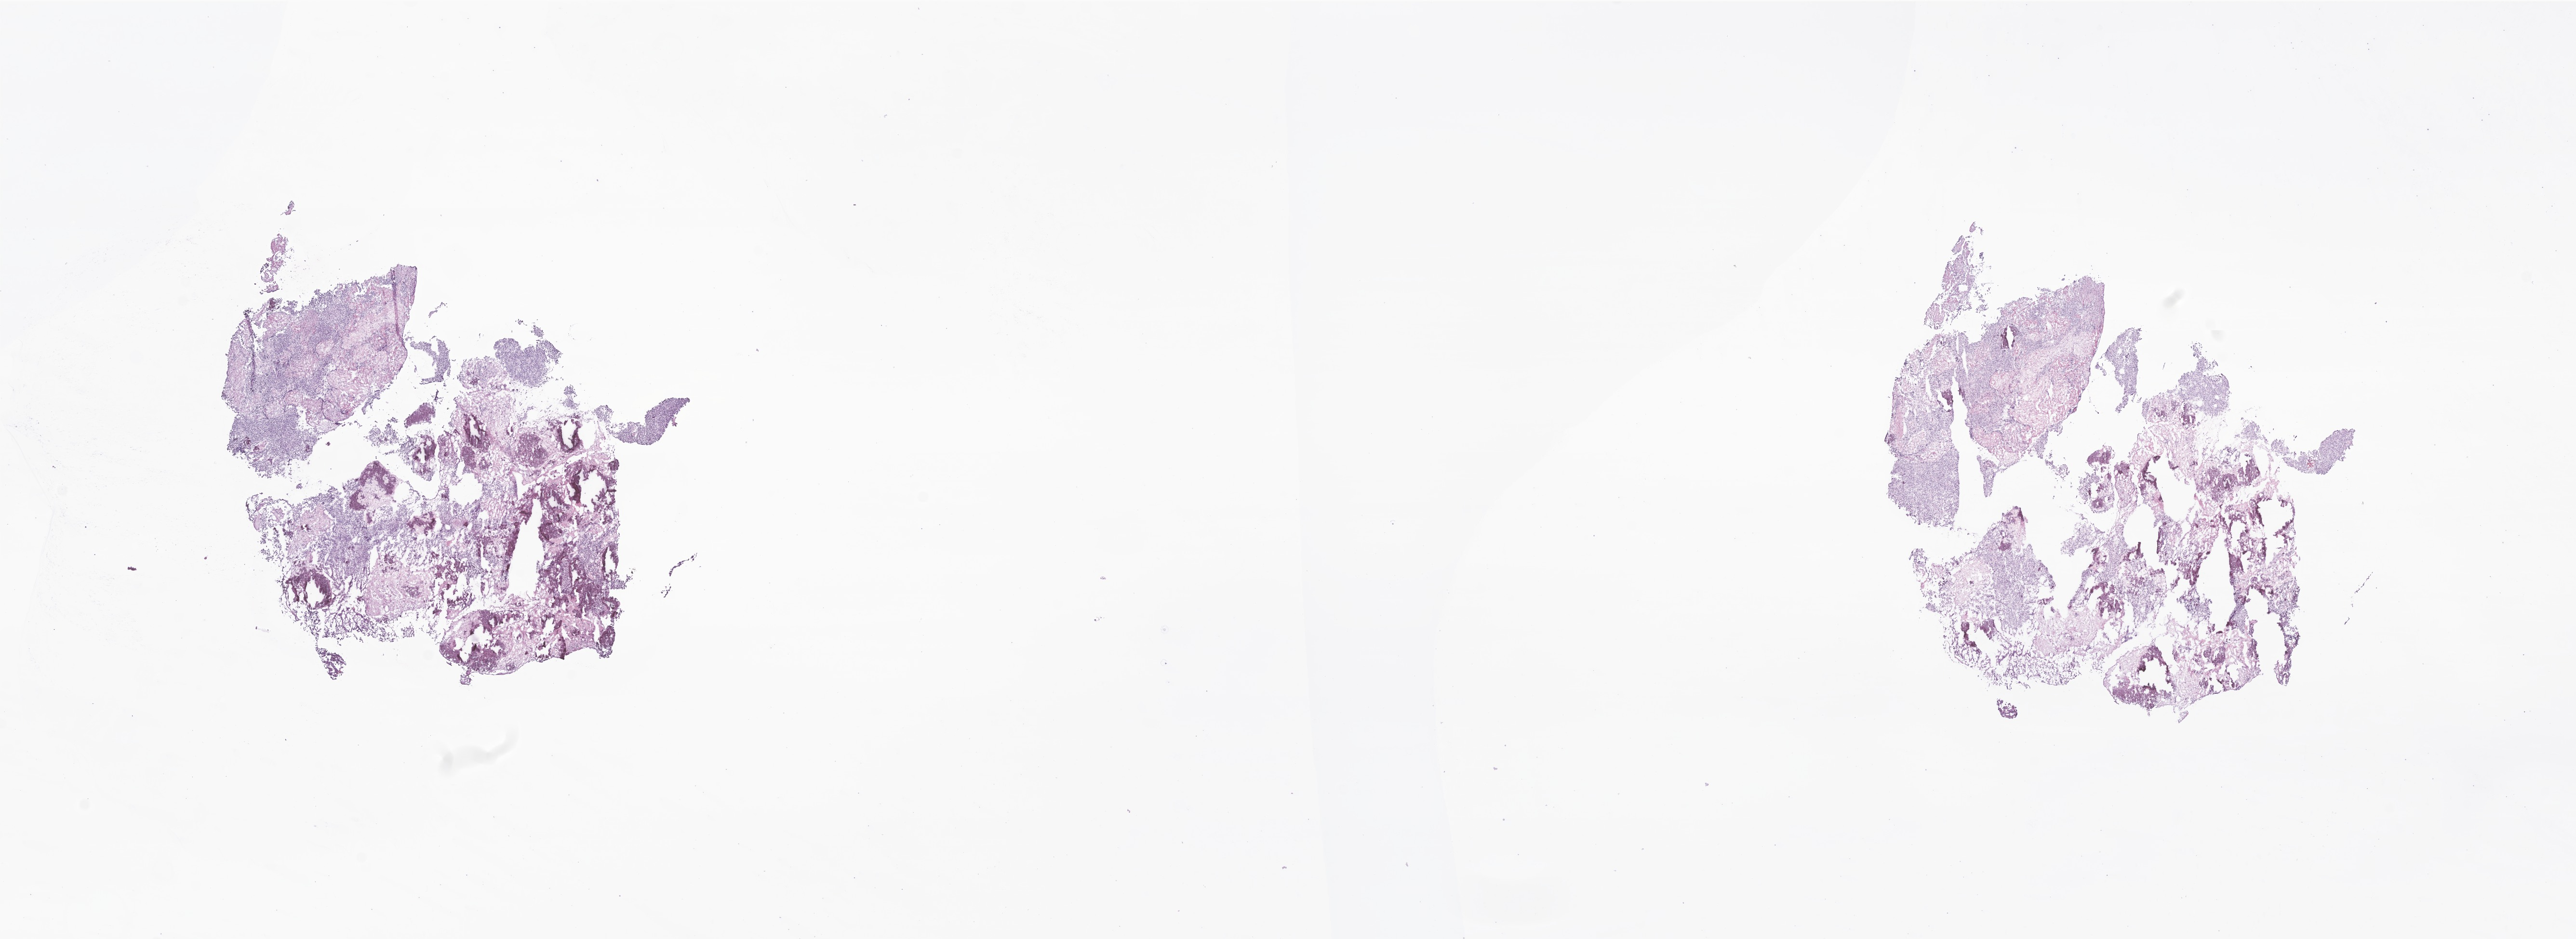
Whole-slide image, hematoxylin and eosin (H&E) stain of tumor tissue from the brain, whole scanned area (about 22.5 x 8.2 mm) shown as a low-resolution overview. Frozen section. Male patient, age 87 months (7 years 3 months).
Diagnosis (ICD-O-3 morphology term): Medulloblastoma, NOS.